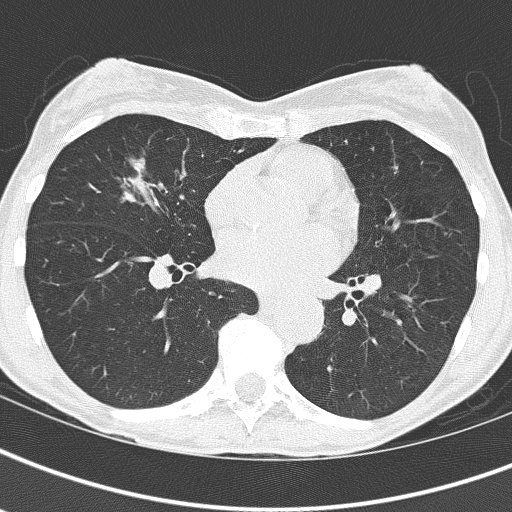
Axial slice from a low-dose chest CT screening exam. Baseline annual screen. Lung window (W 1500 / L -600 HU). Slice 90 of 161 in the series. Female participant, aged 67 years at enrolment. Current smoker at enrolment.
Expert reader's lesion annotation, bounding box (x1, y1, x2, y2) in pixels: (91, 139, 175, 218). No non-calcified nodule or mass ≥4 mm was recorded by the screening reader at this exam. Official screen result: negative screen, significant abnormalities not suspicious for lung cancer. Lung cancer was diagnosed 832 days after this screen (after the third annual screen): bronchiolo-alveolar adenocarcinoma, NOS, right middle lobe, well differentiated (G1), stage IA (AJCC 6th edition), 25 mm at pathology.